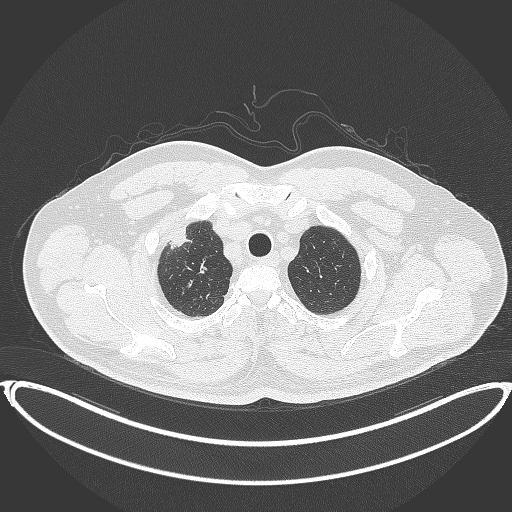
Chest CT, one axial slice; slice 343 of 399 in the series (ordered by position); reconstruction kernel B70f; 120 kVp; lung window (W 1500 / L -600 HU); 1 mm slice thickness; 512 × 512 image matrix. Male patient, age 53 years. Case-level facts recorded for this patient, not image findings: clinical TNM (as recorded): T2a N0 M0.
Outlined on this slice (bounding box drawn by a radiologist):
- lung tumour (recorded histology: adenocarcinoma): bounding box (x1, y1, x2, y2) in pixels: (168, 218, 194, 253)